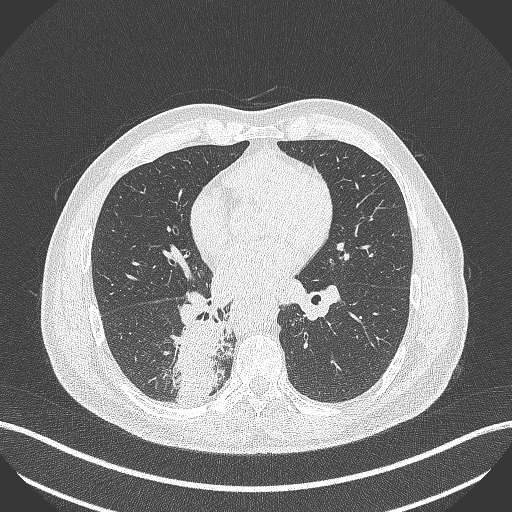
Chest CT, one axial slice. Reconstruction kernel B70f. Lung window (W 1500 / L -600 HU). 1 mm slice thickness. 512 × 512 image matrix. Male patient, age 61 years. From the clinical record (not read from this slice): clinical TNM (as recorded): T1 N0 M0.
Structures marked on this image (rectangle marked by the reading radiologist):
- lung tumour (recorded histology: small cell carcinoma): bounding box (x1, y1, x2, y2) in pixels: (173, 318, 235, 414)